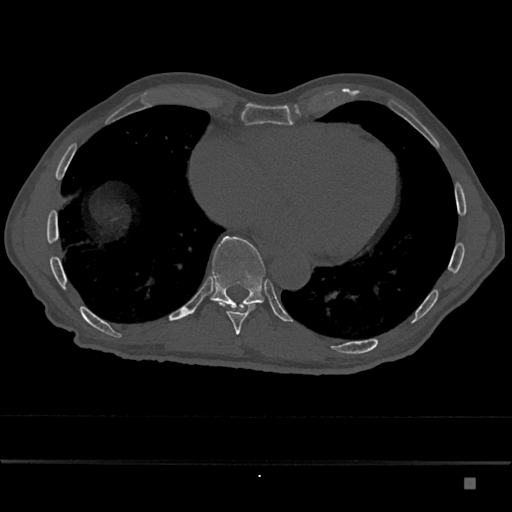
CT including the spine, one axial slice. Position 774 of 797 along the scan axis. Reconstruction kernel Br40s/3. 120 kVp. Bone window (W 1800 / L 400 HU). 0.5 mm slice thickness. 512 × 512 image matrix, field of view 390 × 390 mm. Male patient, age 72 years. From the clinical record (not read from this slice): primary cancer: prostate.
Structures marked on this image (semi-automatically segmented with operator editing):
- T10 vertebra: bounding box (x1, y1, x2, y2) in pixels: (210, 236, 266, 310)
- T9 vertebra: (220, 303, 255, 335)